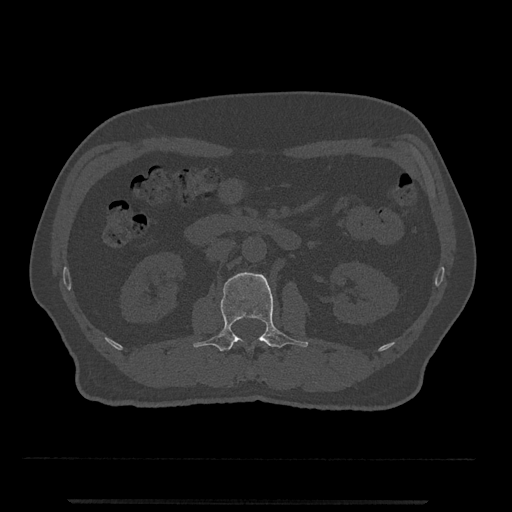
CT including the spine, one axial slice. Position 276 of 797 along the scan axis. 120 kVp. Bone window (W 1800 / L 400 HU). 0.5 mm slice thickness. 512 × 512 image matrix. Male patient, age 63 years. From the clinical record (not read from this slice): primary cancer: prostate.
Structures marked on this image (semi-automatically segmented with operator editing):
- L2 vertebra: bounding box [x1, y1, x2, y2] px = [193, 272, 309, 351]